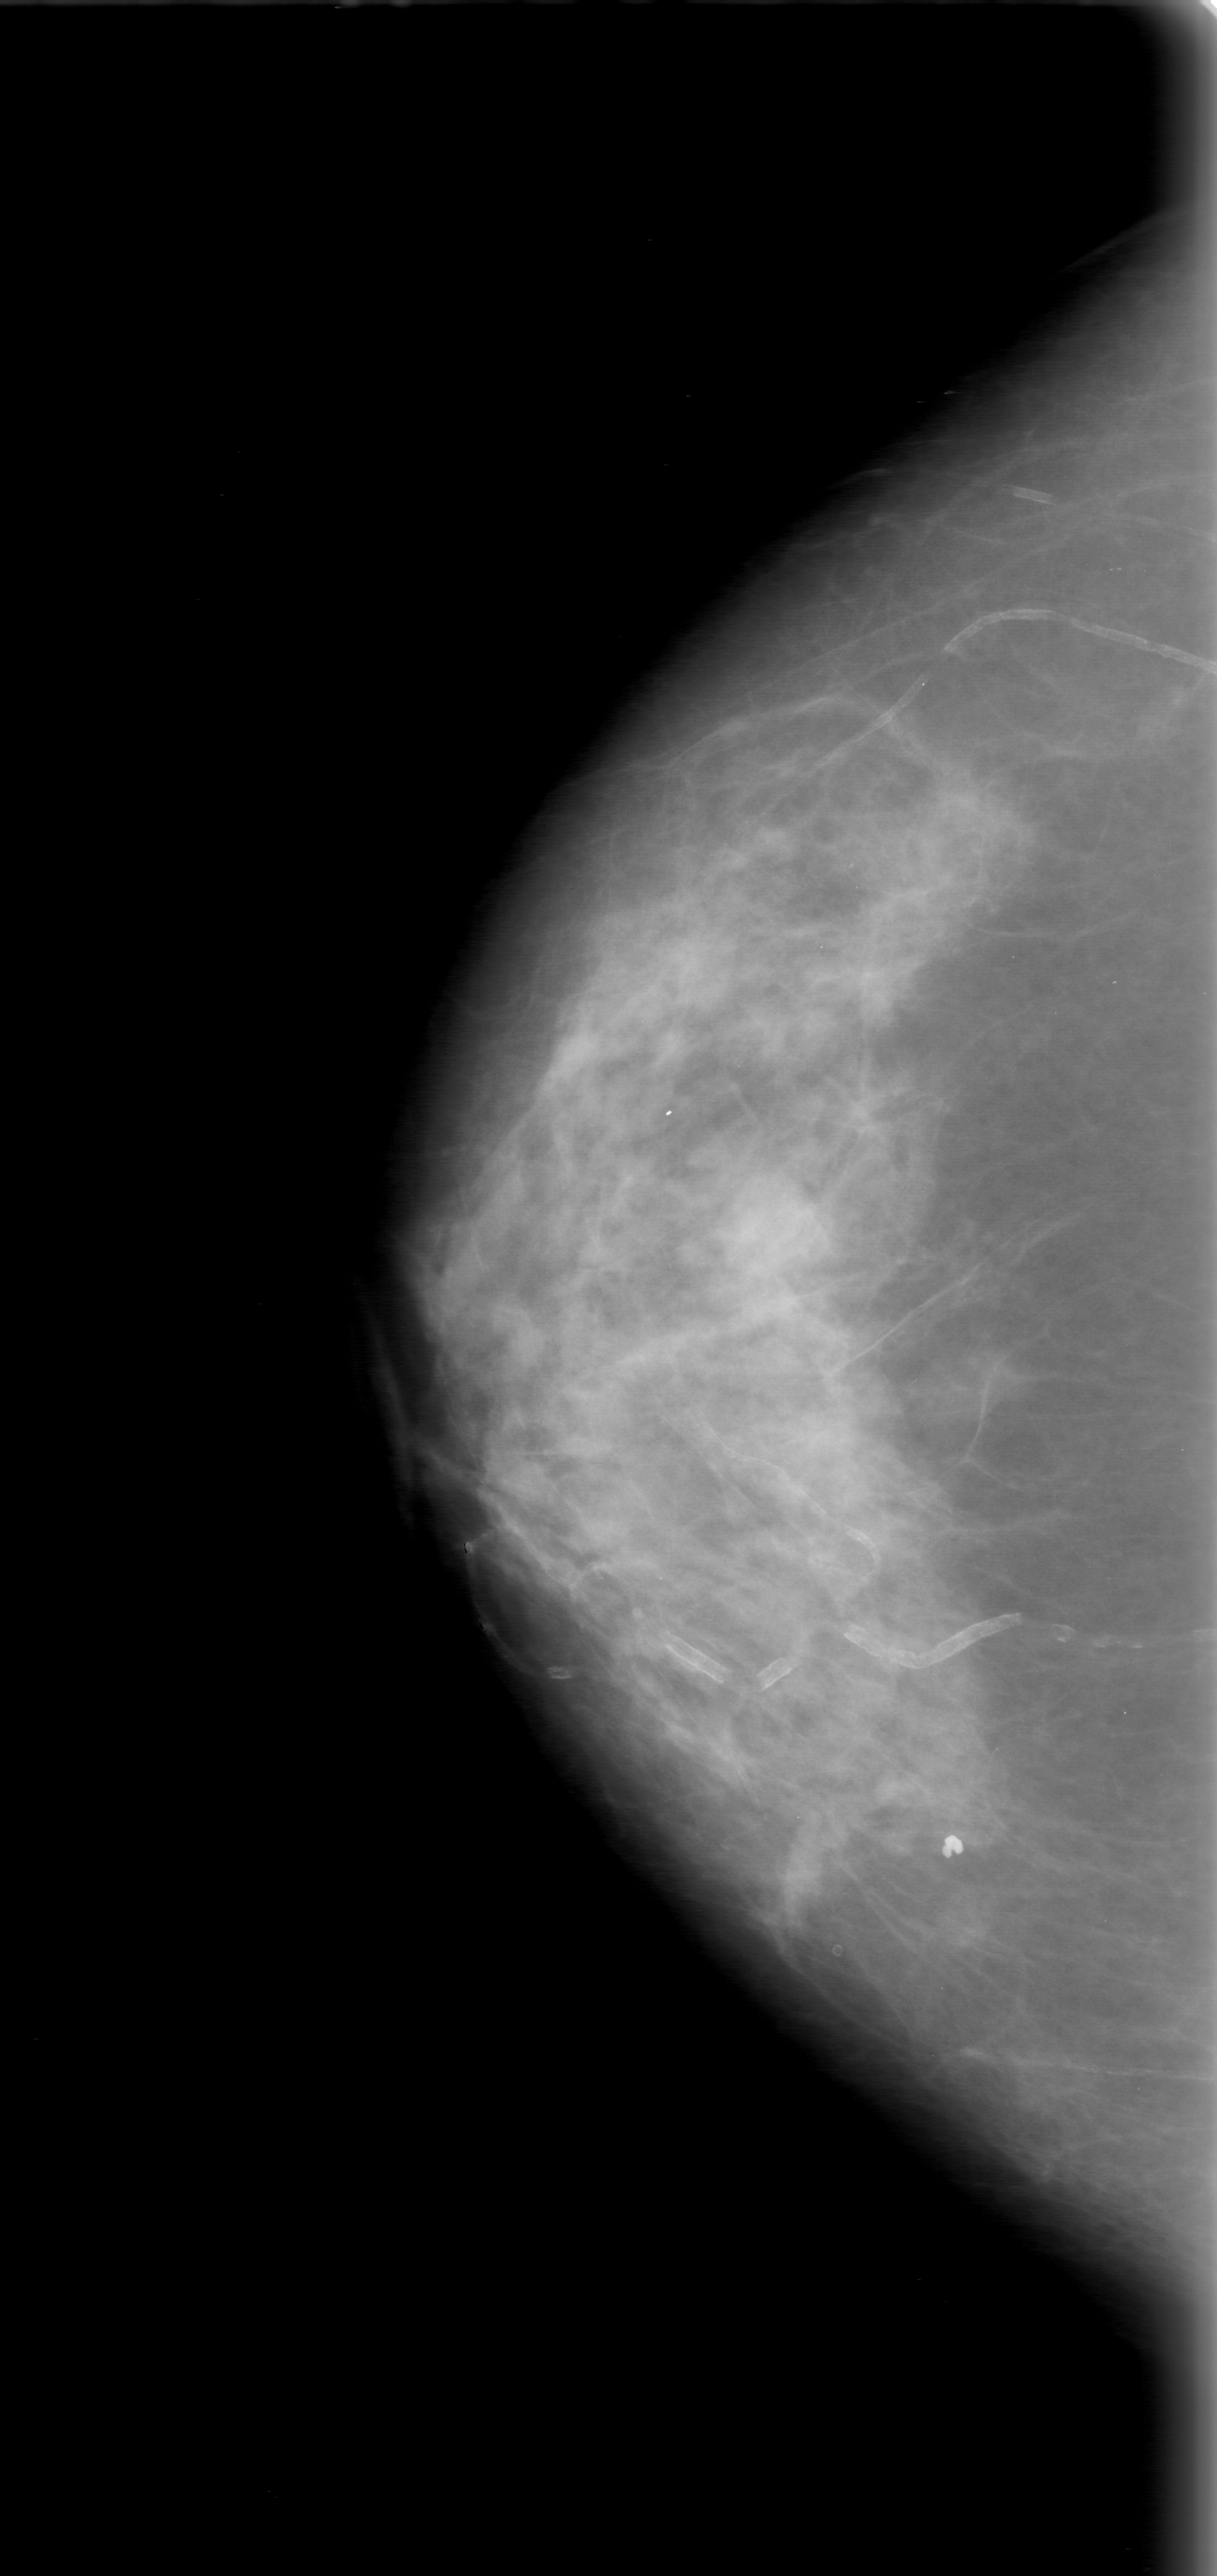
Scanned film-screen mammogram; right breast; CC view; breast composition: scattered fibroglandular densities (BI-RADS density category 2 of 4); 1217 × 2576 image matrix.
Marked abnormalities (boxes around the expert regions of interest):
- mass, shape round, margins obscured; BI-RADS assessment category 0 (incomplete: needs additional imaging); subtlety rating 4 on a 1 (subtle) to 5 (obvious) scale; pathology (as recorded): benign: bounding box (x1, y1, x2, y2) in pixels: (702, 1150, 851, 1295)